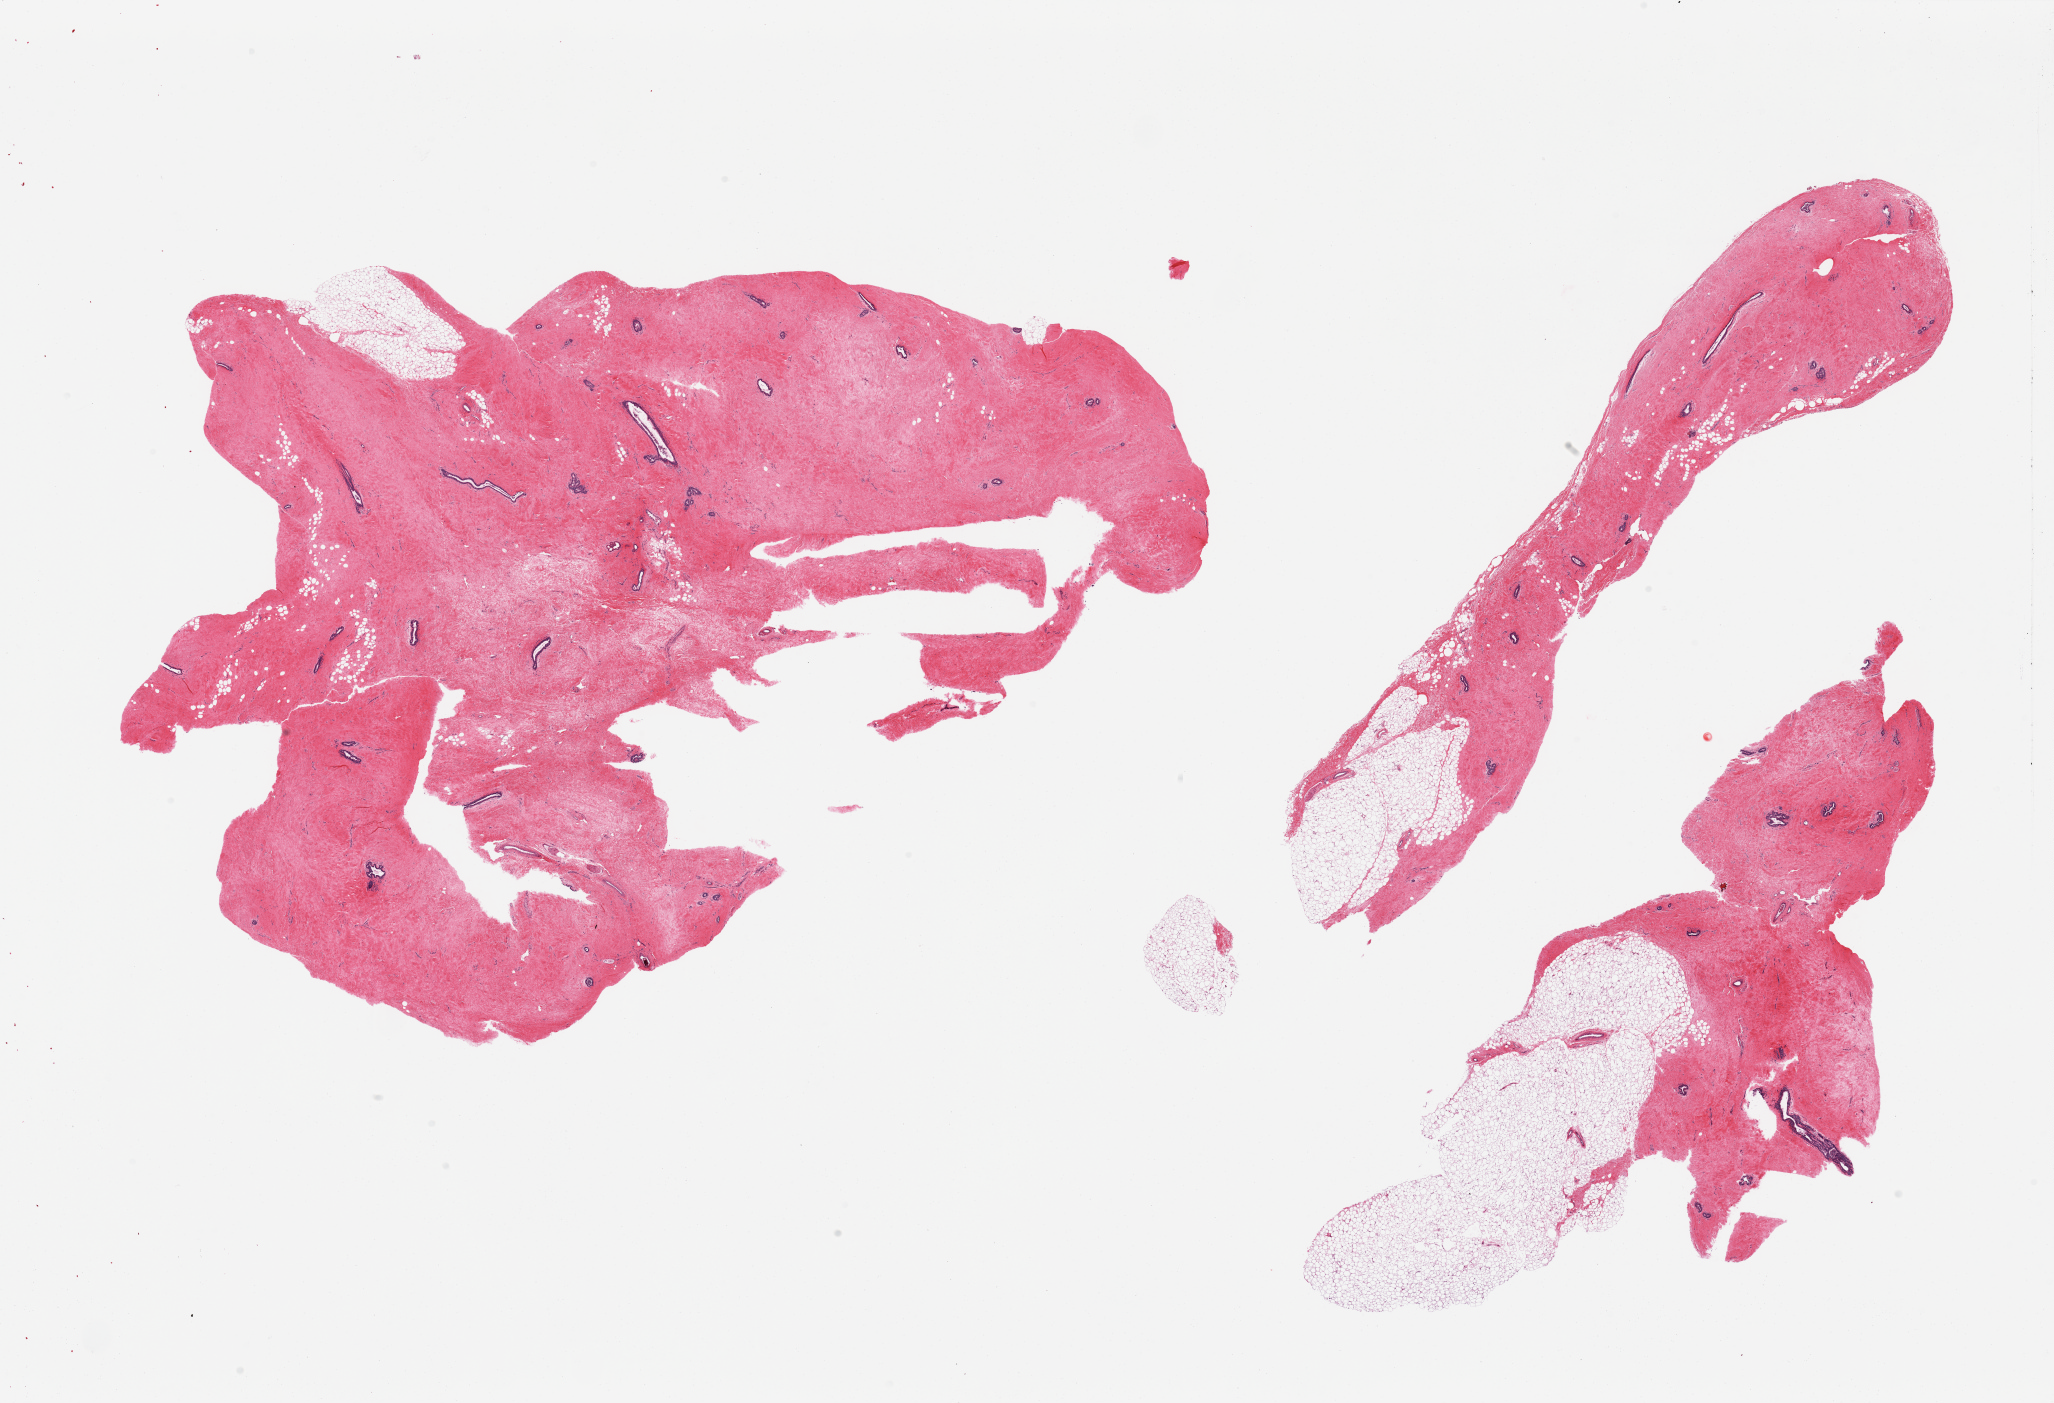
Whole-slide image, H&E stain, a low-resolution overview of the entire scanned area, about 32.5 x 22.2 mm (acquisition: 20x scan). PAXgene-fixed paraffin-embedded (PFPE) section. Sampled site (target tissue): breast. Tissue donor sample. Male donor.
* pathologist's review note for this sample: 3 pieces, gynecomastoid change and focal apocrine metaplasia